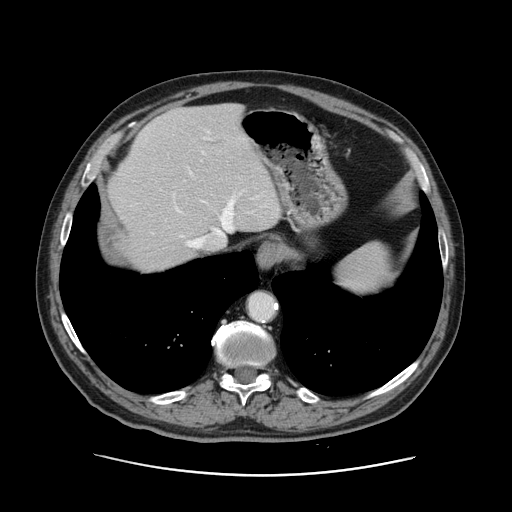
Contrast-enhanced abdominal CT, one axial slice; slice 107 of 141 in the series (ordered by position); intravenous contrast given; soft-tissue window (W 400 / L 40 HU); 2.5 mm slice thickness; 512 × 512 image matrix. Male patient, age 72 years. From the clinical record (not read from this slice): diagnosis: colorectal cancer liver metastases, imaged before liver resection; multiple liver metastases: yes; largest metastasis: 5.4 cm.
Annotated regions visible in this slice (outlined manually by an expert reader):
- hepatic veins: bounding box (x1, y1, x2, y2) in pixels: (175, 131, 254, 248)
- liver: (109, 103, 281, 273)
- planned liver remnant (the part of the liver to remain after resection): (138, 103, 281, 273)
- portal vein (with intrahepatic branches): (204, 135, 231, 220)